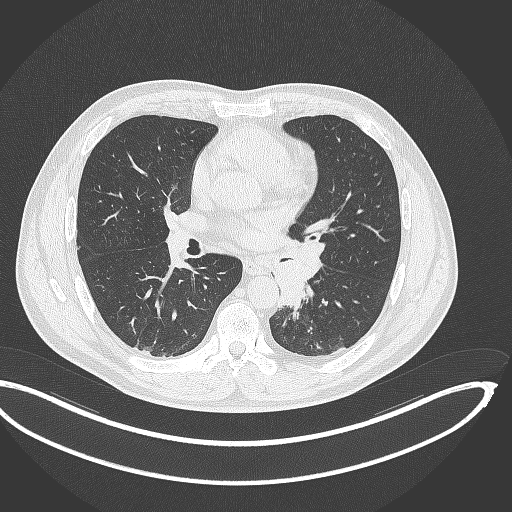
Chest CT, one axial slice. Position 184 of 362 along the scan axis. Reconstruction kernel B70f. 120 kVp. Lung window (W 1500 / L -600 HU). 1 mm slice thickness. 512 × 512 image matrix. Male patient, age 50 years. From the clinical record (not read from this slice): clinical TNM (as recorded): T2a N3 M0.
Structures marked on this image (bounding box drawn by a radiologist):
- lung tumour (recorded histology: squamous cell carcinoma): bounding box <269,236,327,307> (left, top, right, bottom; pixels)